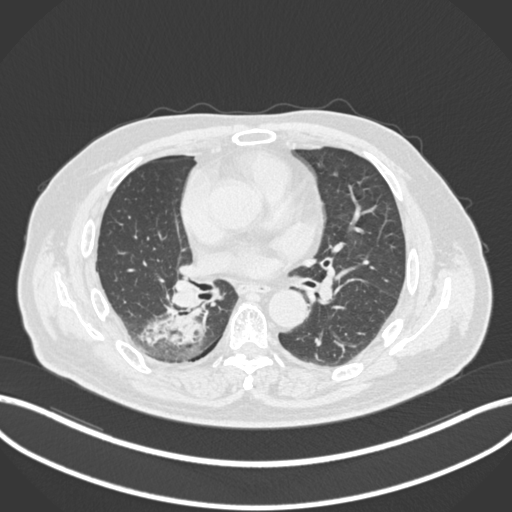
Chest CT, one axial slice. Slice 95 of 218 in the series (ordered by position). Reconstruction kernel B30f. Lung window (W 1500 / L -600 HU). 1 mm slice thickness. 512 × 512 image matrix. Male patient, age 68 years. From the clinical record (not read from this slice): clinical TNM (as recorded): T2a N0 M0.
Annotated regions visible in this slice (bounding box drawn by a radiologist):
- lung tumour (recorded histology: adenocarcinoma): bounding box (x1, y1, x2, y2) in pixels: (141, 305, 213, 355)